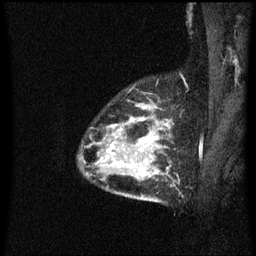
Breast MRI (dynamic contrast-enhanced), one sagittal slice; dynamic contrast-enhanced series, image 2 of 3 at this slice position (ordered by acquisition); 1.5 T; TE 4.2 ms, TR 8.4 ms; 2 mm slice thickness; 256 × 256 image matrix, field of view 200 × 200 mm. Female patient, age 34 years. From the clinical record (not read from this slice): setting: breast cancer imaged before/during neoadjuvant chemotherapy; receptor status: HR-positive, HER2-negative.
Outlined on this slice (semi-automatic segmentation, software-assisted and operator-edited):
- analysis volume of interest (the breast-tissue region the enhancement analysis was run in; not a lesion): bounding box (x1, y1, x2, y2) in pixels: (80, 104, 171, 203)
- tumour enhancement mask (voxels above the 70 % enhancement threshold inside the analysis volume of interest): (107, 118, 161, 175)